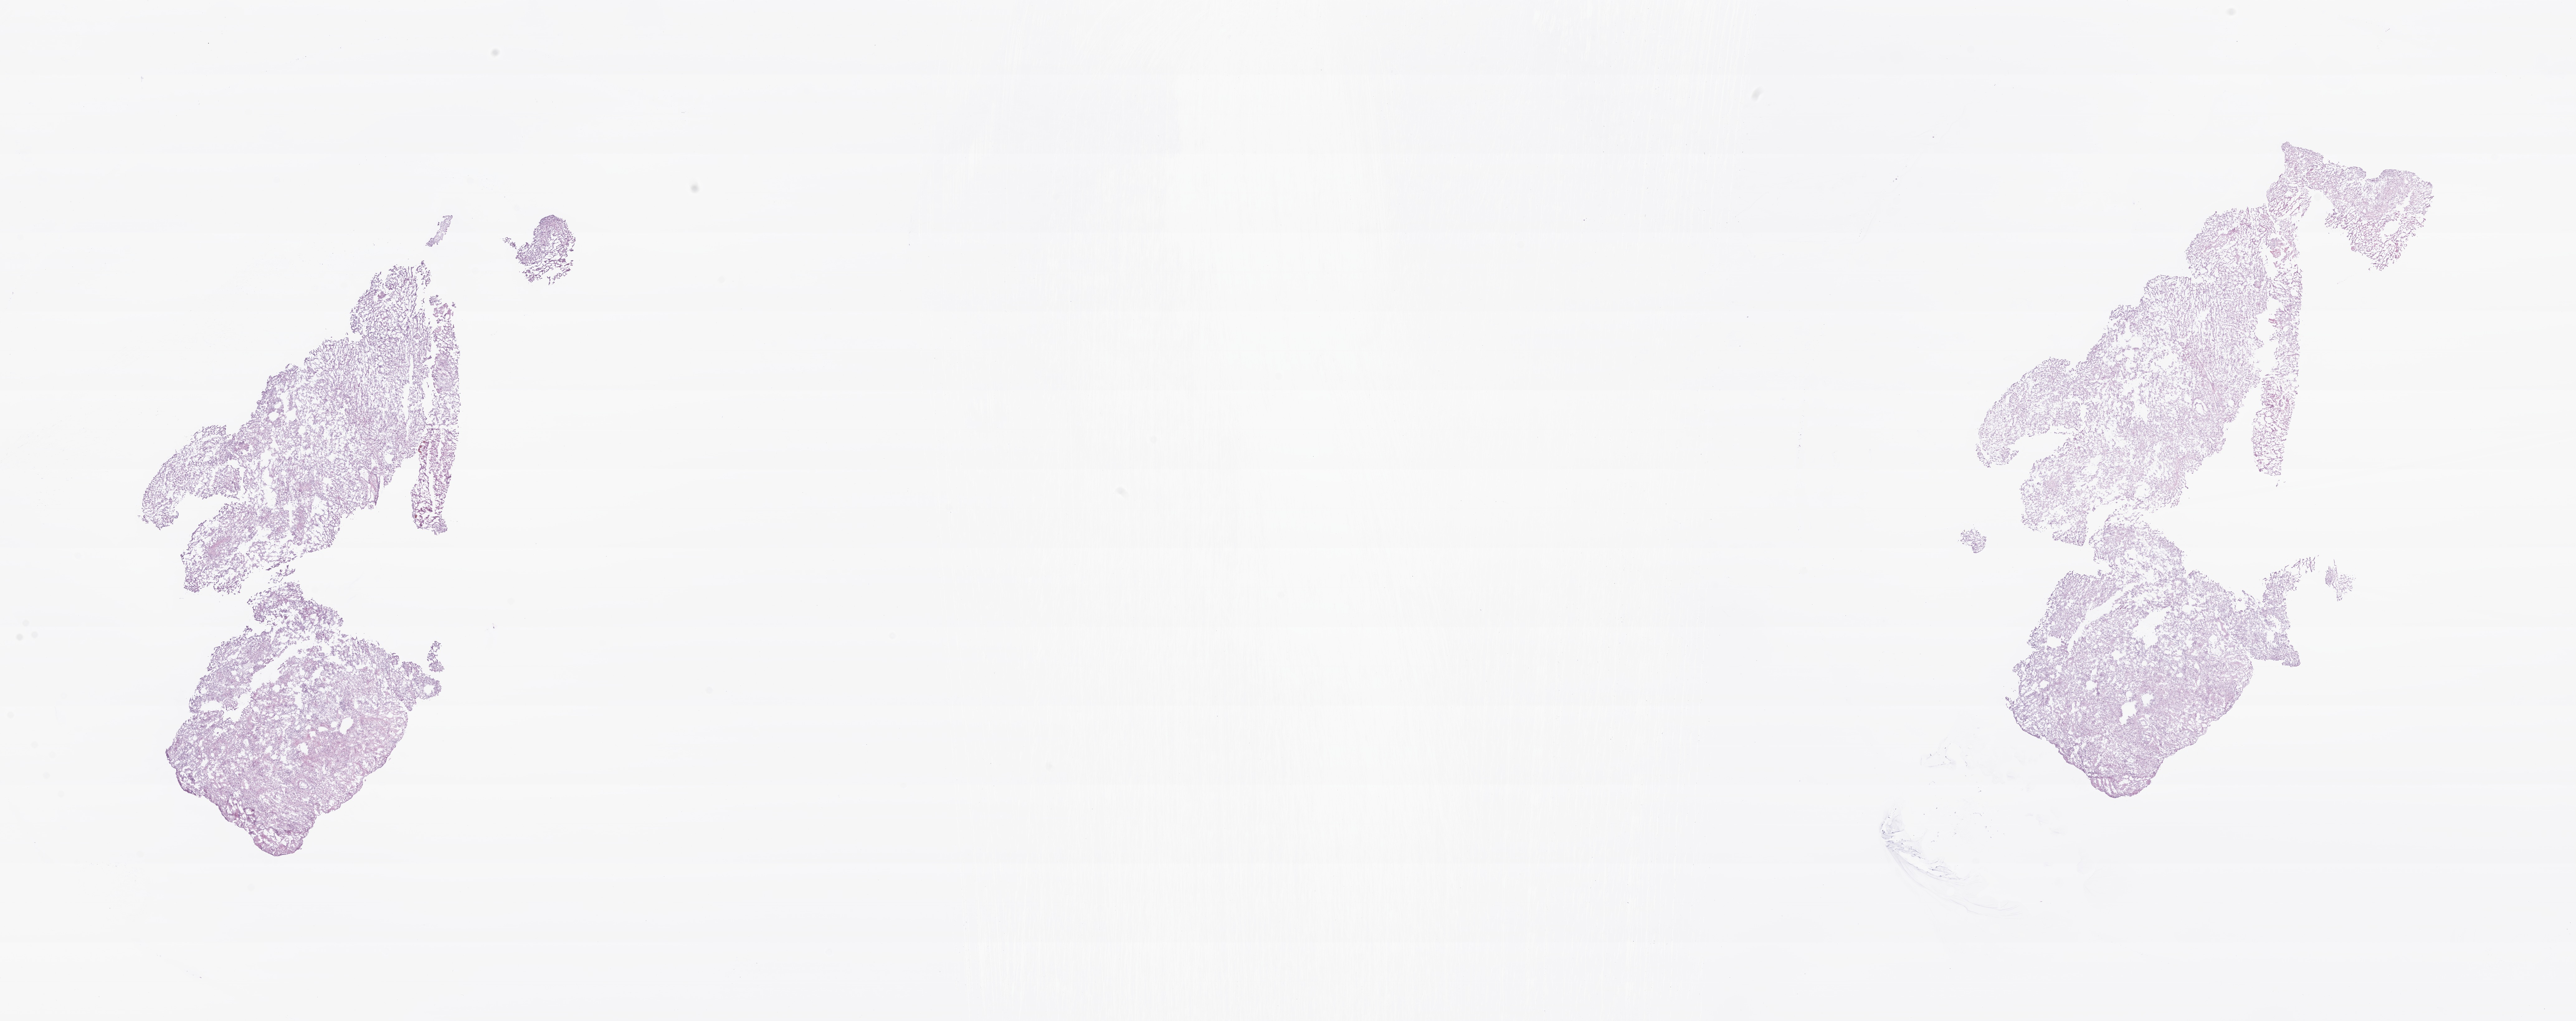
Digitized H&E-stained section of tumor tissue from the brain — shown as a low-resolution overview of the whole scanned area (about 34.8 x 13.8 mm). Cryosection (OCT / tissue freezing medium). Male patient, age 168 months (14 years).
* diagnosis: Glioma, malignant